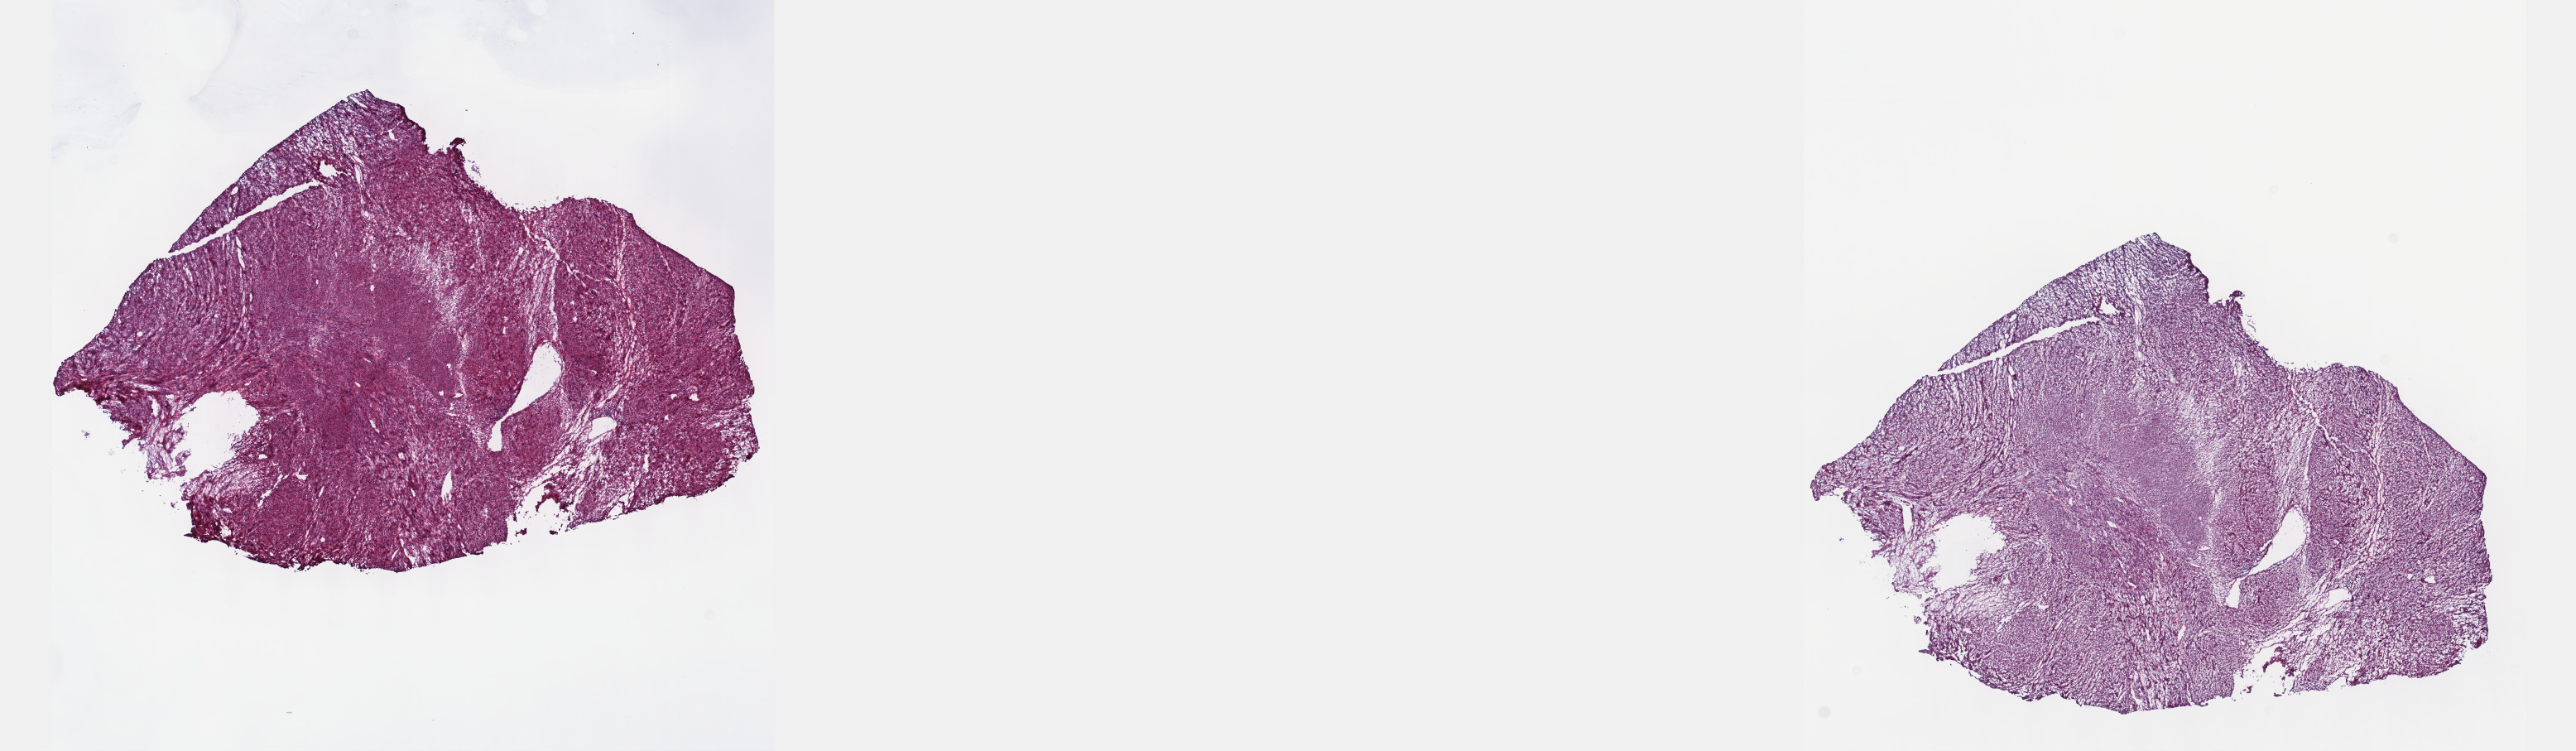
H&E whole-slide image — low-resolution overview of the scanned area, about 25.1 x 7.3 mm; frozen section from the top of the tissue portion; sample: primary tumour, retroperitoneum and peritoneum. Male, age 33 years at initial diagnosis.
Histologic diagnosis: Leiomyosarcoma, NOS (retroperitoneum).